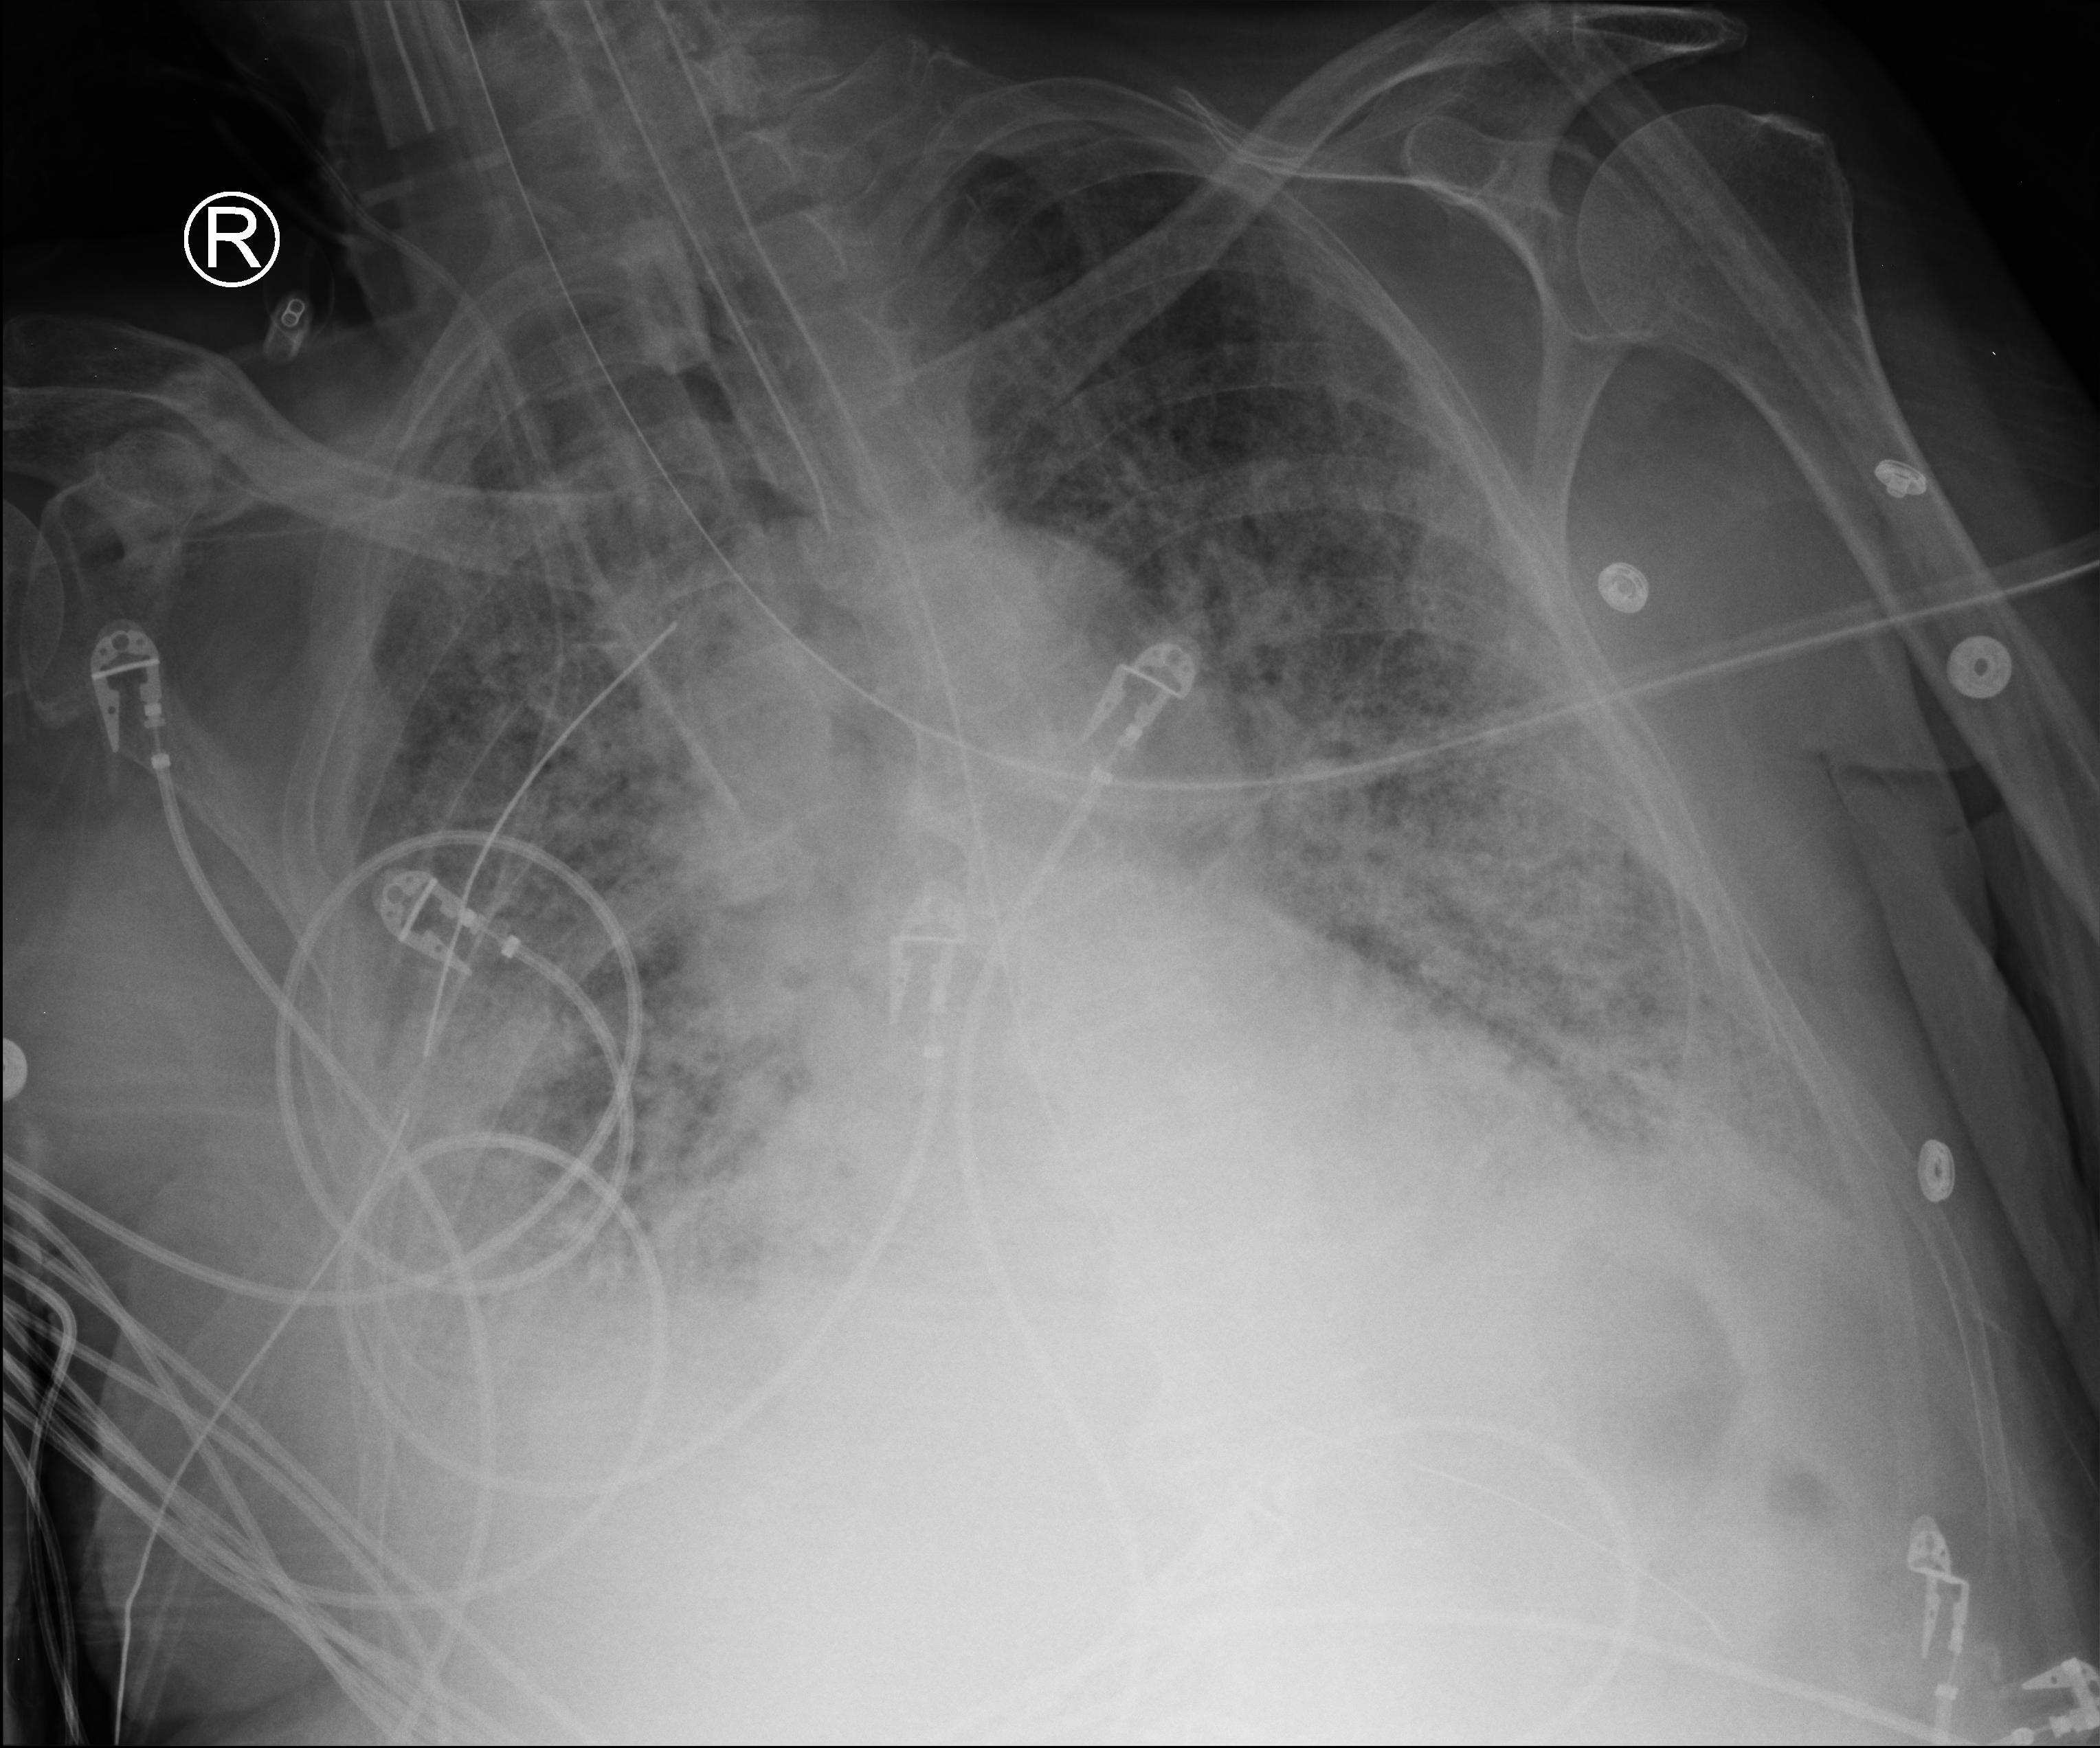
Bedside chest radiograph (computed radiography); anteroposterior (AP) projection. Male patient hospitalised with COVID-19, age 75–90 years.
Hospital-stay facts (about this admission, not read from this image; timing relative to this image not recorded): mechanically ventilated during this hospital stay: yes; length of hospital stay: 47 days; COPD (admission record): no.